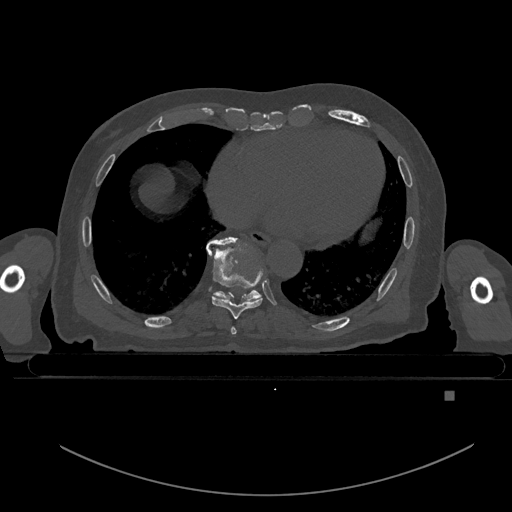
CT including the spine, one axial slice; position 187 of 969 along the scan axis; bone window (W 1800 / L 400 HU); 0.5 mm slice thickness; 512 × 512 image matrix, field of view 456 × 456 mm. Male patient, age 82 years. Case-level facts recorded for this patient, not image findings: primary cancer: prostate.
Annotated regions visible in this slice (semi-automatically segmented with operator editing):
- T7 vertebra: bounding box (x1, y1, x2, y2) in pixels: (231, 326, 236, 335)
- T8 vertebra: (209, 240, 263, 319)
- T9 vertebra: (206, 236, 261, 301)